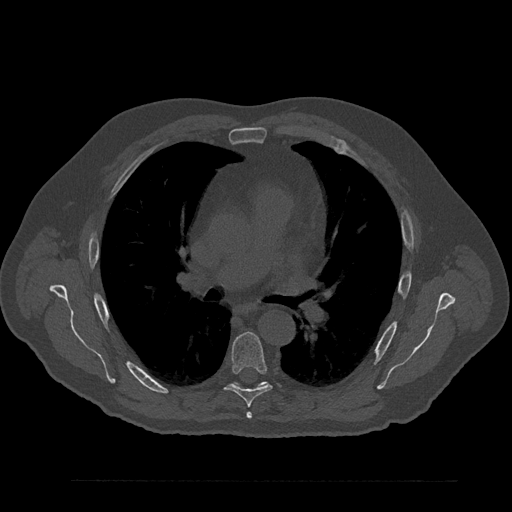
CT including the spine, one axial slice. Slice 551 of 797 in the series (ordered by position). Reconstruction kernel Br40s/3. 120 kVp. Bone window (W 1800 / L 400 HU). 0.5 mm slice thickness. 512 × 512 image matrix. Male patient, age 61 years. Case-level facts recorded for this patient, not image findings: primary cancer: prostate.
Structures marked on this image (semi-automatic segmentation, software-assisted and operator-edited):
- T5 vertebra: box from (x=247, y=412) to (x=252, y=418) px
- T6 vertebra: (x=225, y=332)–(x=272, y=408)
- T7 vertebra: (x=235, y=381)–(x=267, y=386)